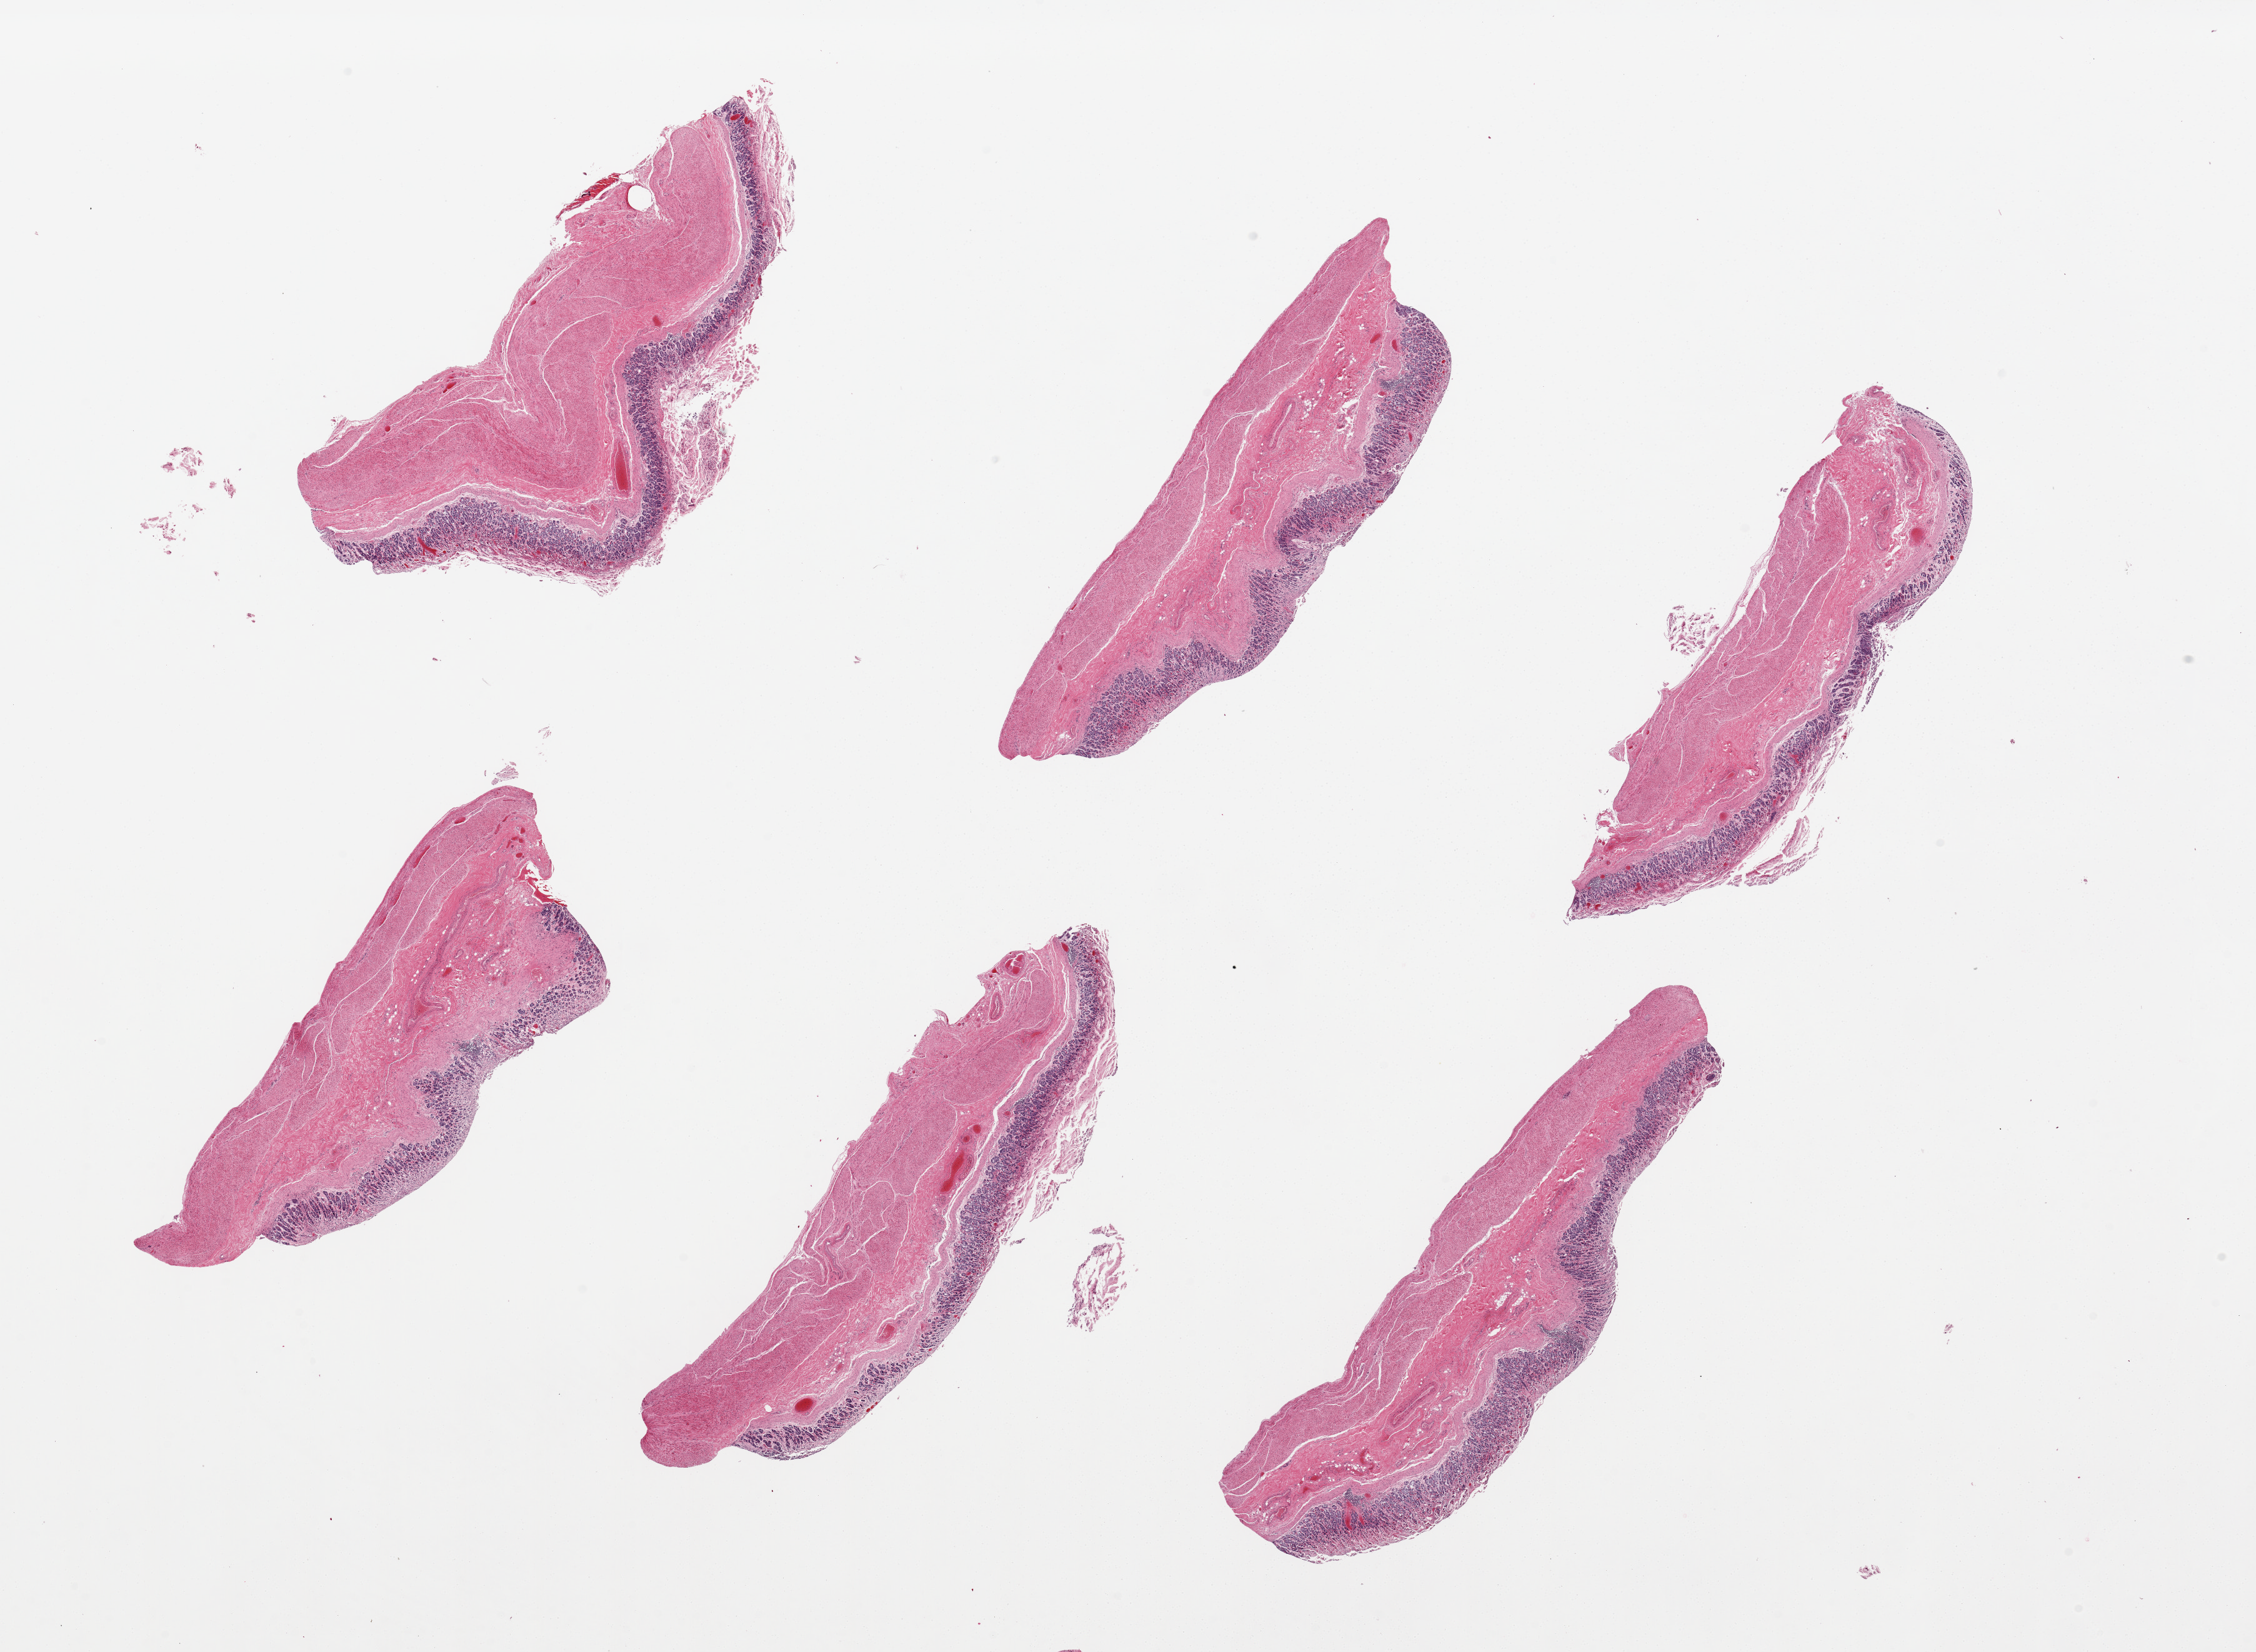
Digitized H&E-stained section, a low-resolution overview of the entire scanned area, about 28.5 x 20.9 mm (from a 20x scan). PAXgene-fixed paraffin-embedded (PFPE) section. Target tissue: stomach. Tissue donor sample. Donor sex: male.
- reviewer comment on this tissue sample: 6 pieces